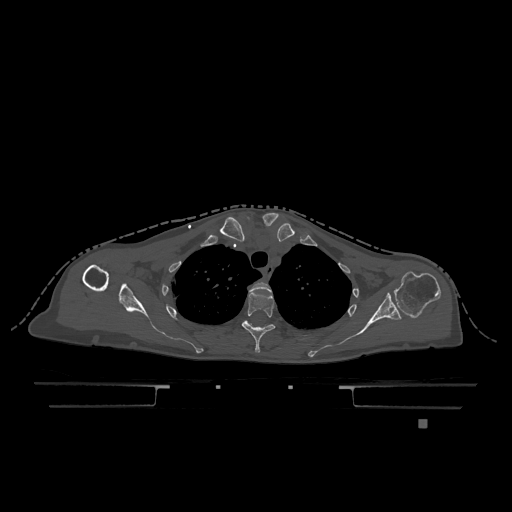
CT including the spine, one axial slice. Slice 922 of 1317 in the series (ordered by position). Bone window (W 1800 / L 400 HU). 0.5 mm slice thickness. 512 × 512 image matrix, field of view 500 × 500 mm. Patient: female, 74 years. Case-level facts recorded for this patient, not image findings: primary cancer: lung; vertebrae with lytic lesions (as recorded): T1, T4, T5, T6, L4, L5.
Annotated regions visible in this slice (semi-automatically segmented with operator editing):
- T2 vertebra: bounding box <249,282,271,292> (left, top, right, bottom; pixels)
- T3 vertebra: <241,291,275,353>
- T4 vertebra: <246,321,306,336>